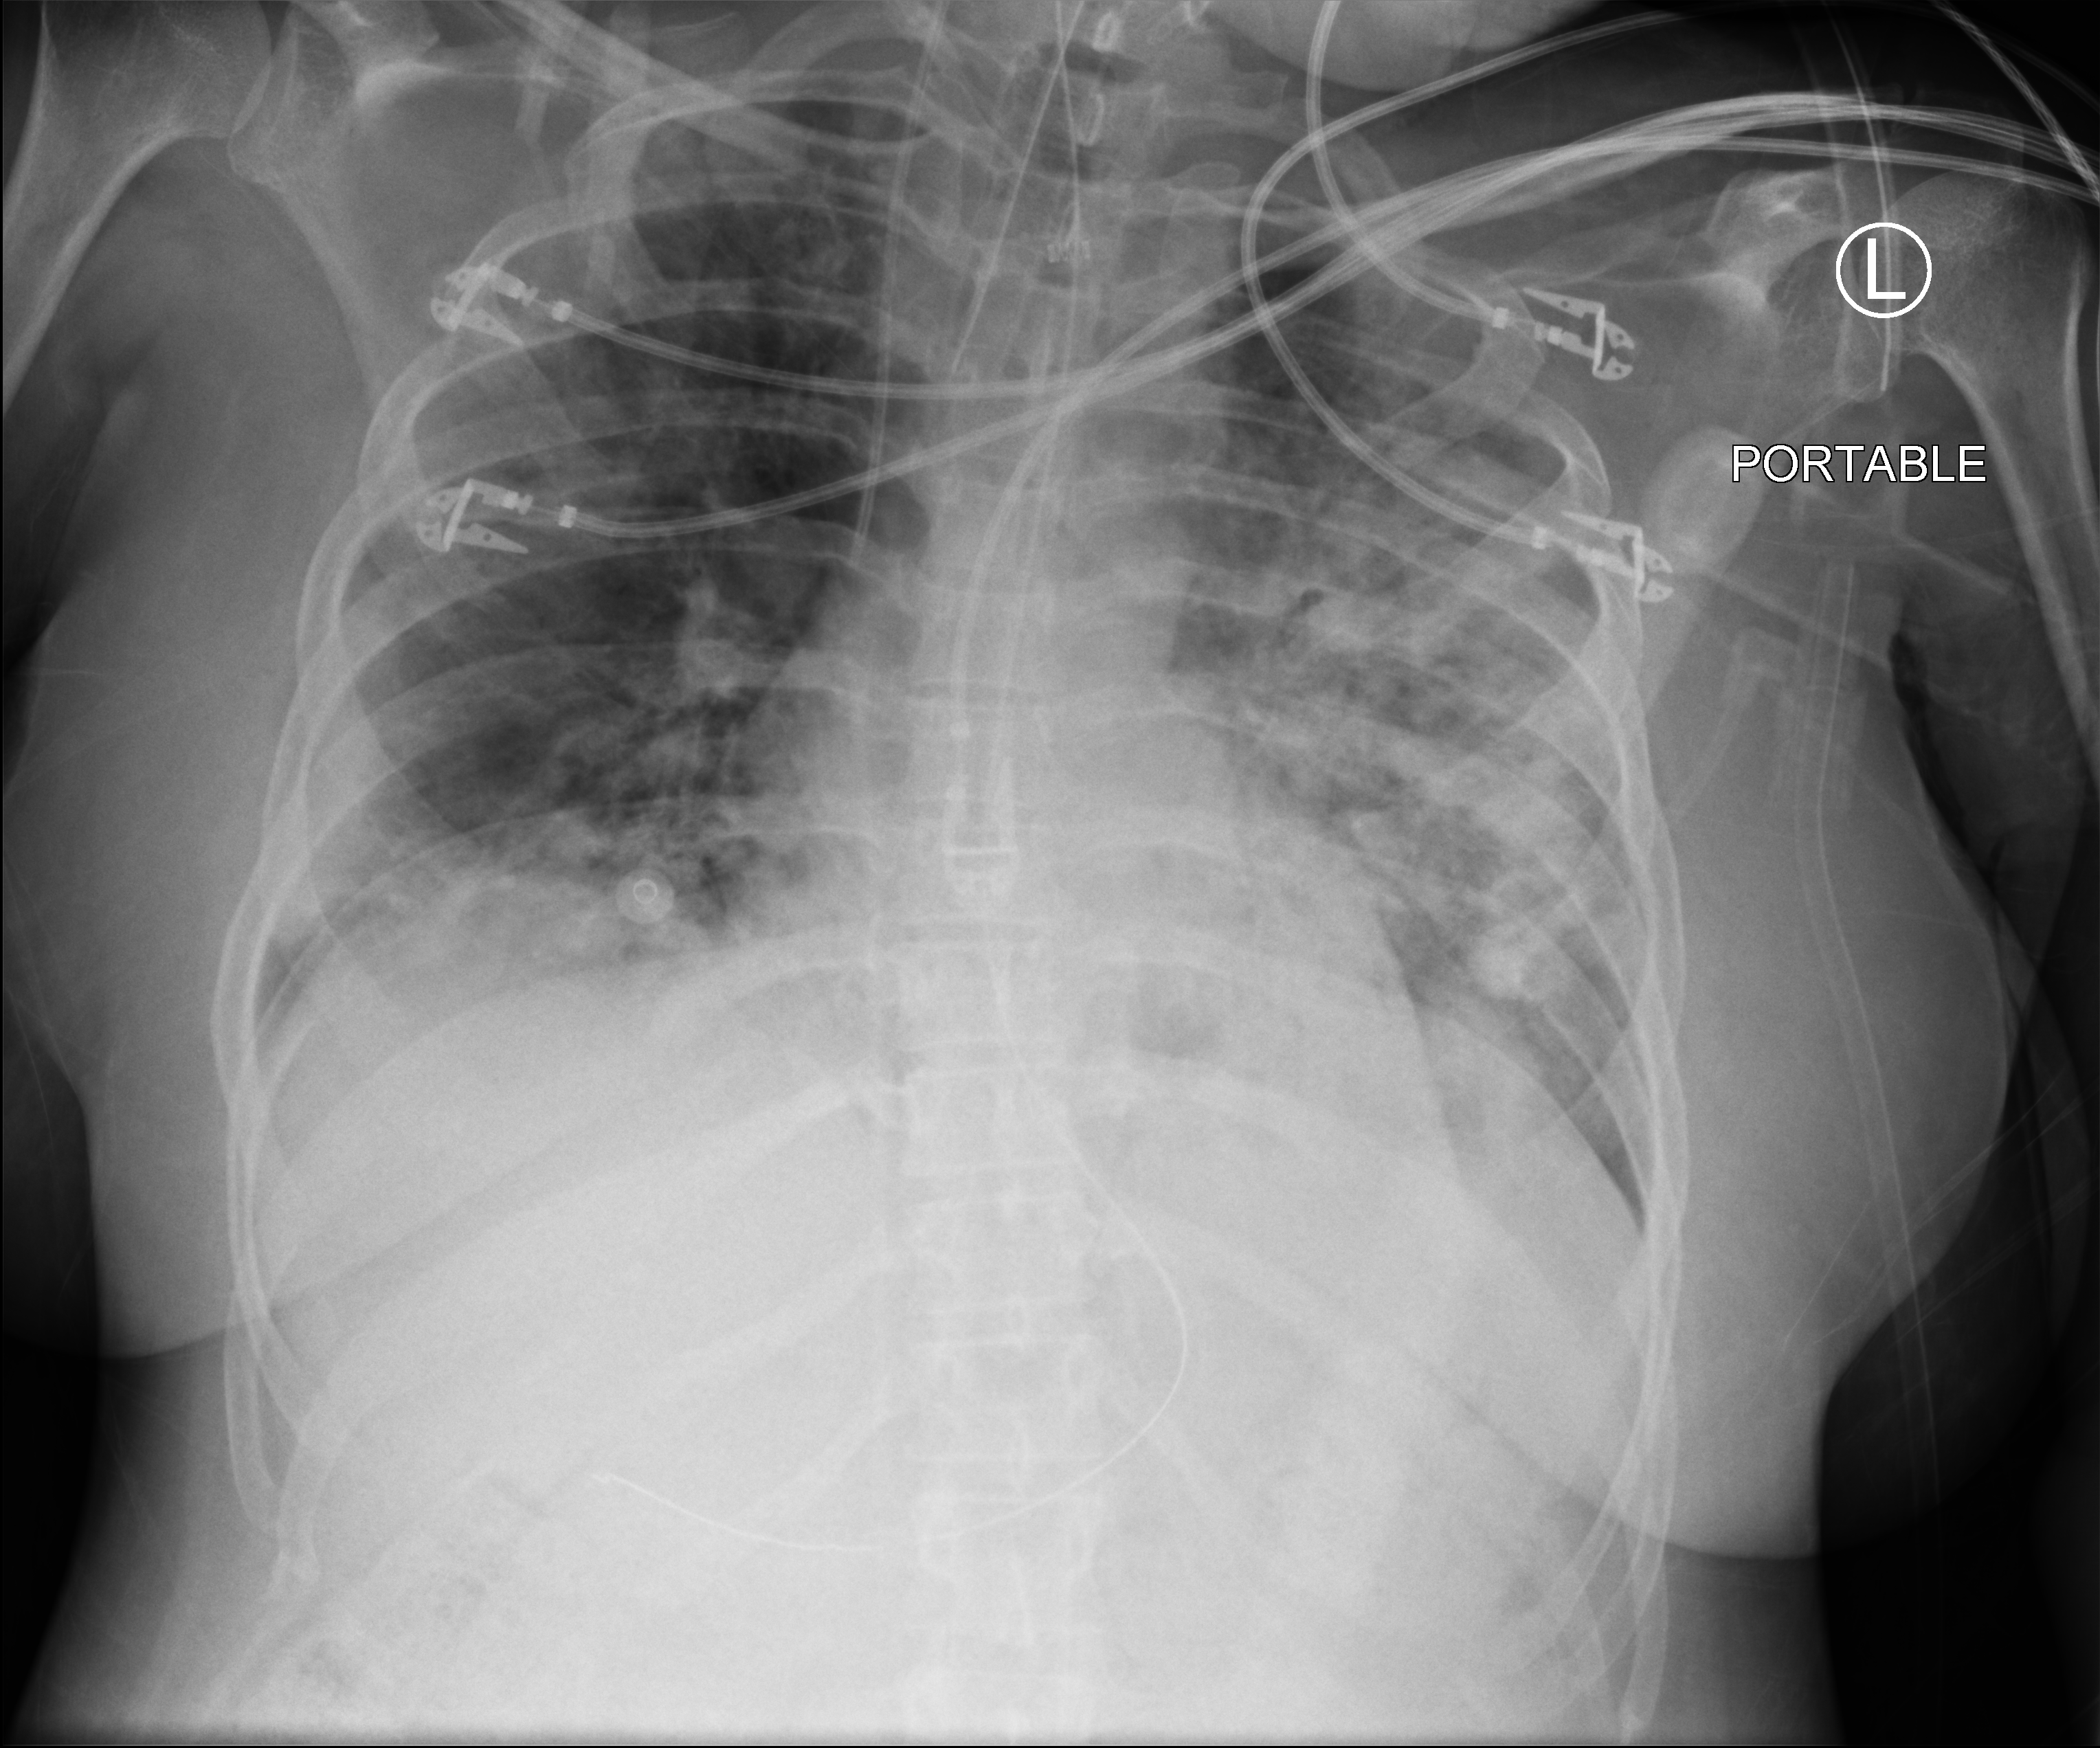
Chest X-ray (portable), anteroposterior (AP) projection. Adult patient hospitalised with COVID-19, age 18–59 years.
Hospital-stay facts (about this admission, not read from this image; timing relative to this image not recorded):
- hypertension (admission record): no